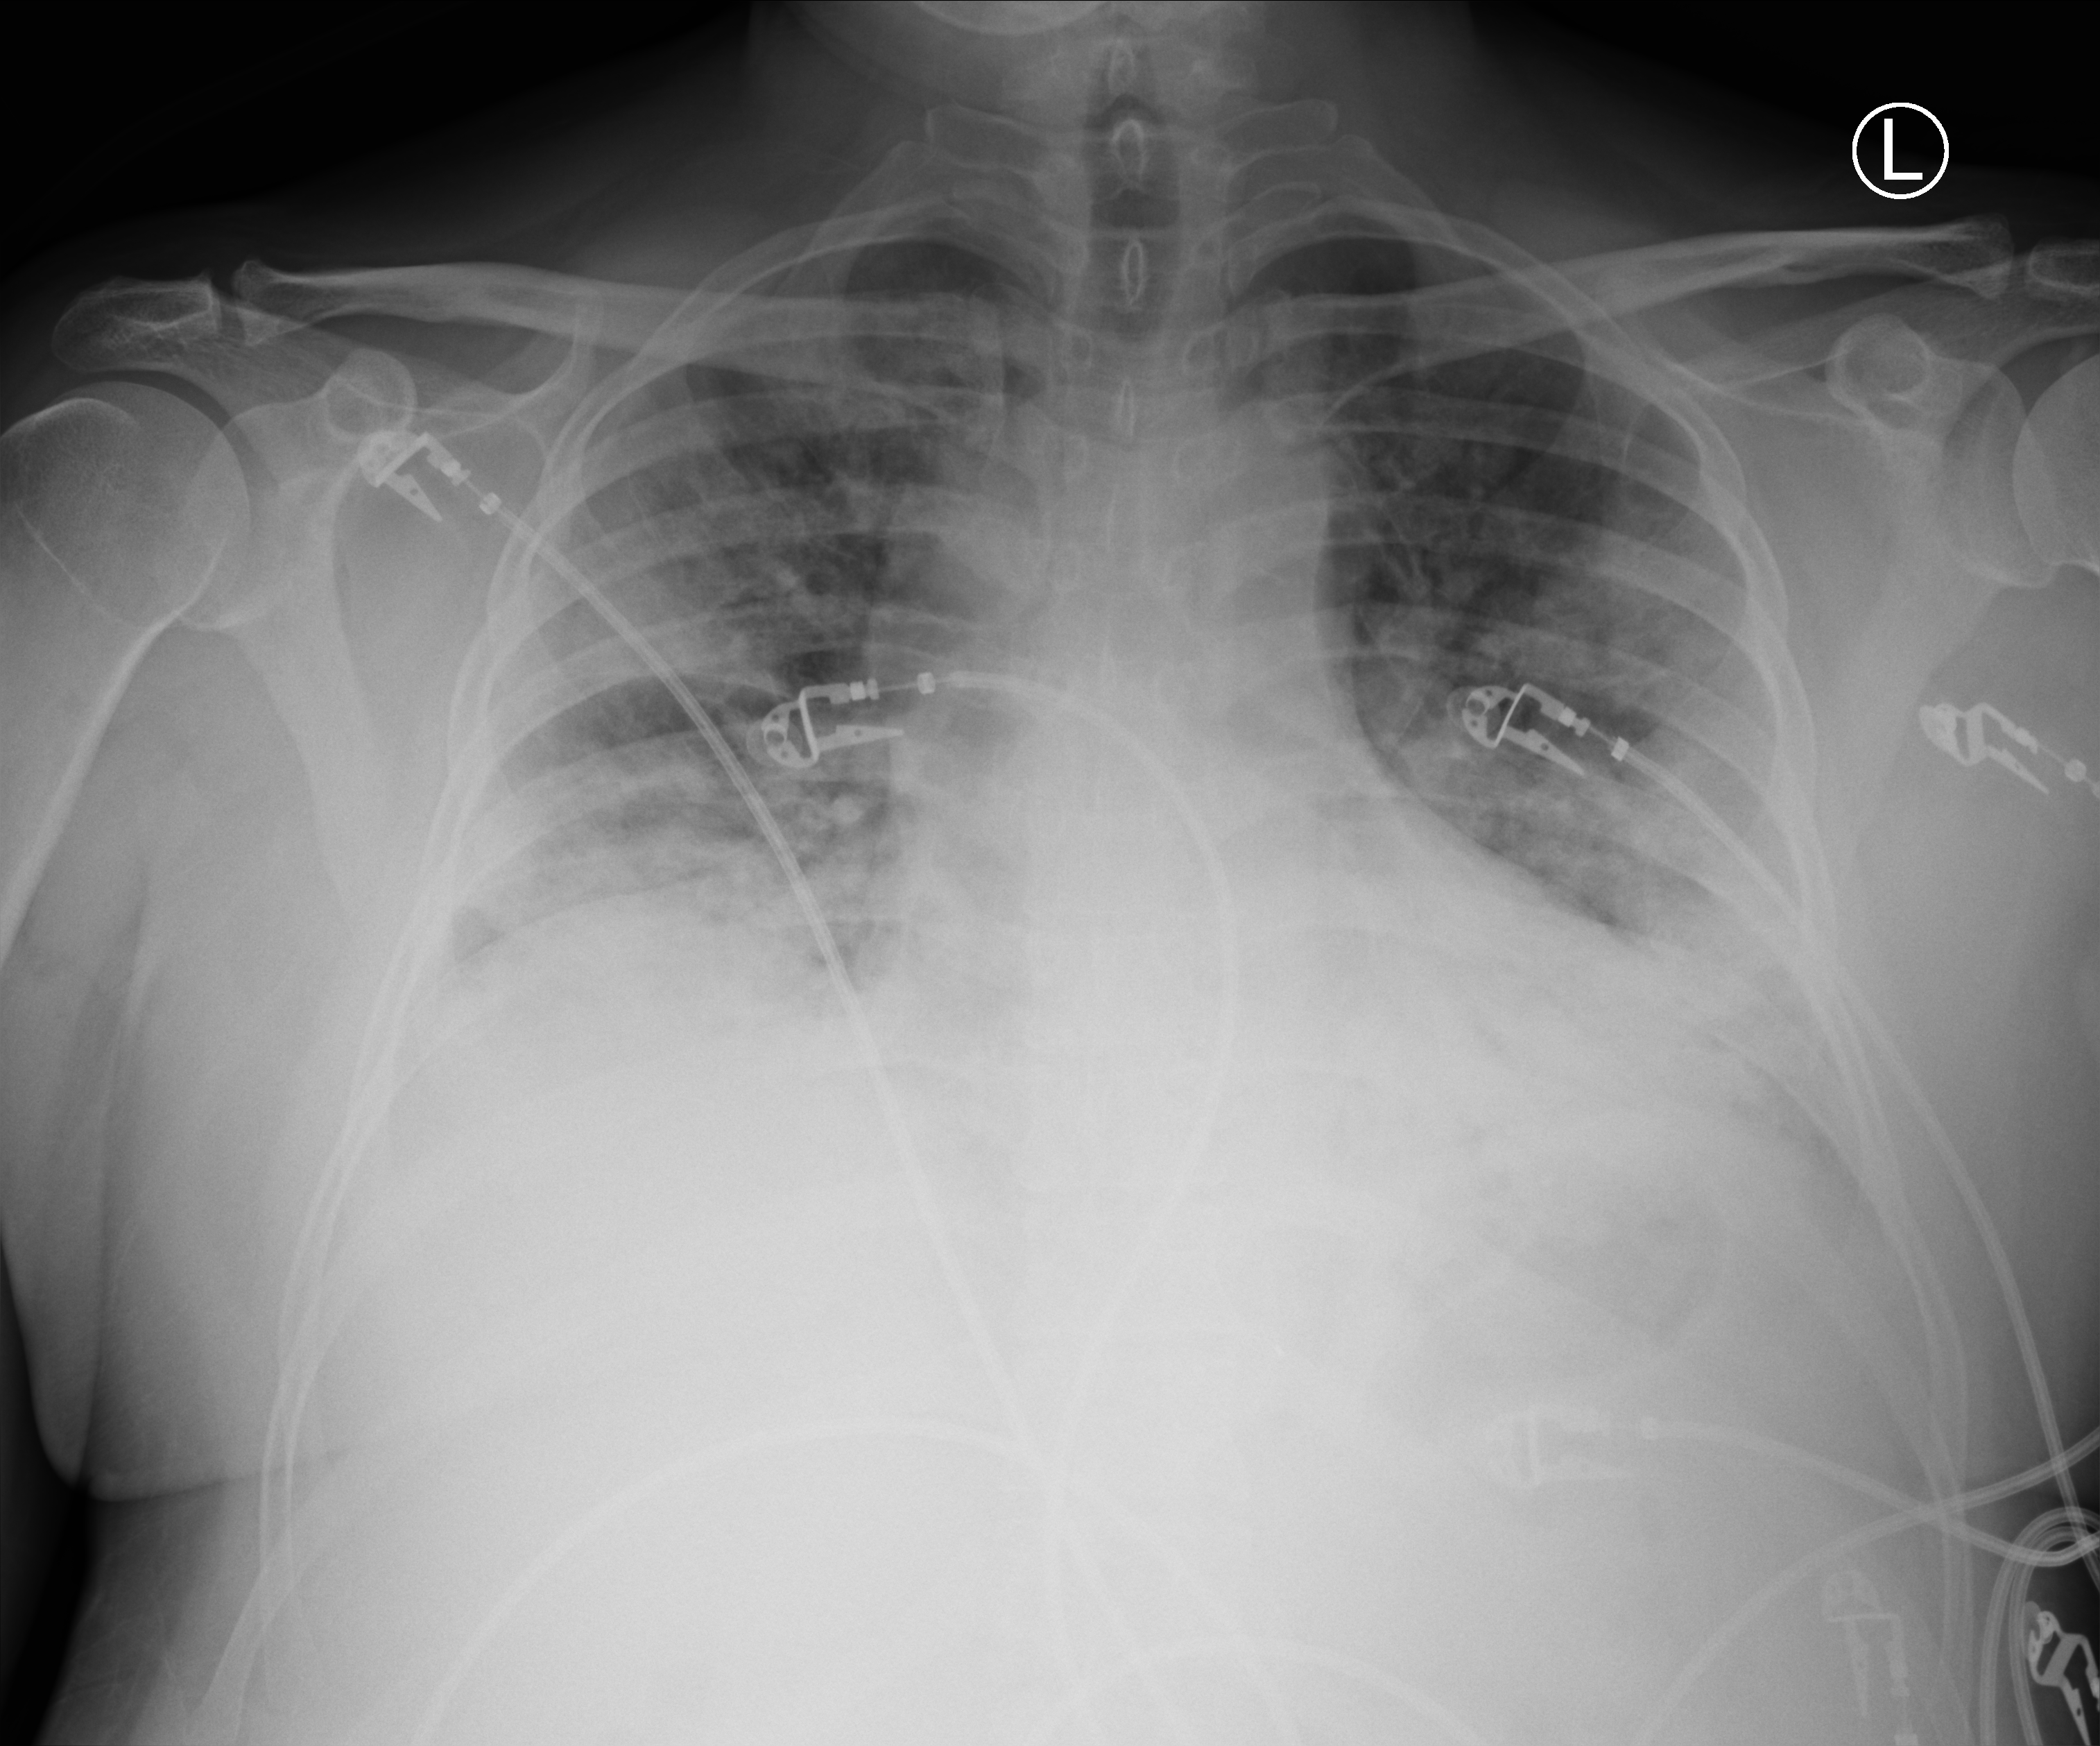
Portable chest radiograph, anteroposterior (AP) projection. Patient hospitalised with COVID-19; male, aged 18–59 years.
Admission-level facts for this patient (not findings on this image; timing relative to this image not recorded):
- mechanically ventilated during this hospital stay: no